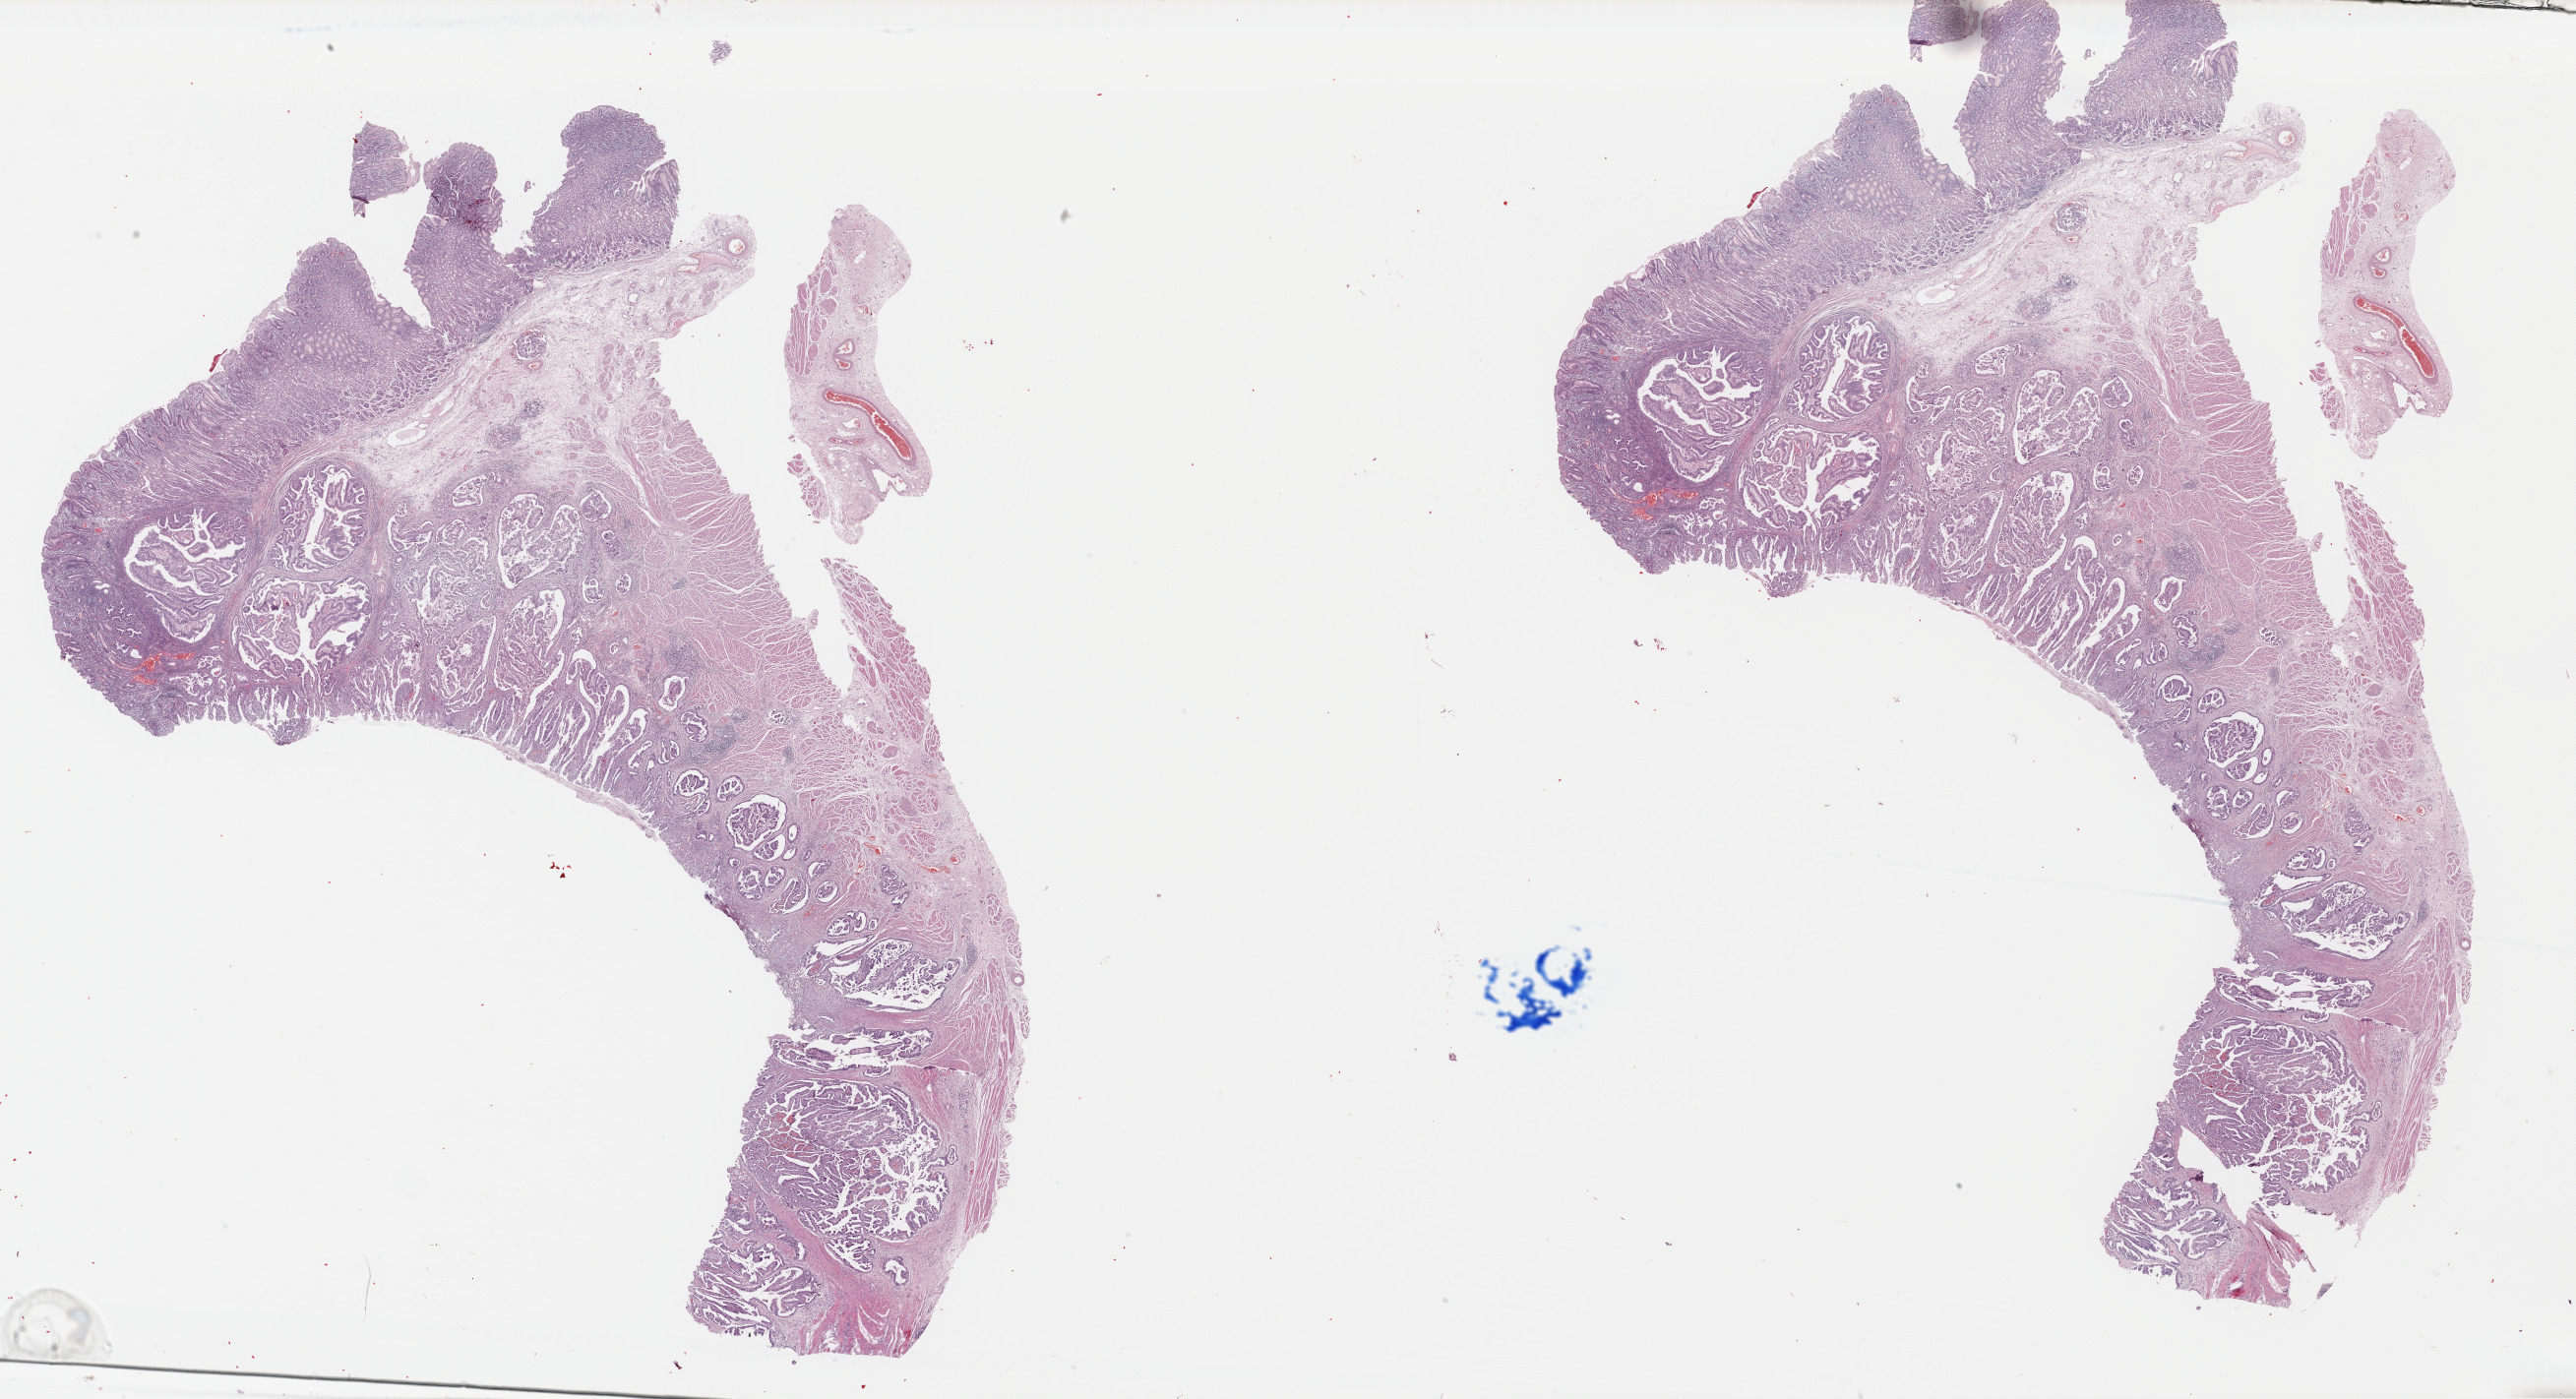
Whole-slide histology image, H&E-stained, shown as a low-resolution overview of the whole scanned area (about 41.2 x 22.4 mm, acquisition: 40x scan), formalin-fixed paraffin-embedded (FFPE) diagnostic section, stomach, primary tumour sample. Male patient; age at initial diagnosis 62 years. Histologic grade: G2 (moderately differentiated).
- diagnosis: Papillary adenocarcinoma, NOS (cardia, NOS)
- AJCC pathologic stage: II
- lymph nodes positive (case pathology): 1 of 14 examined